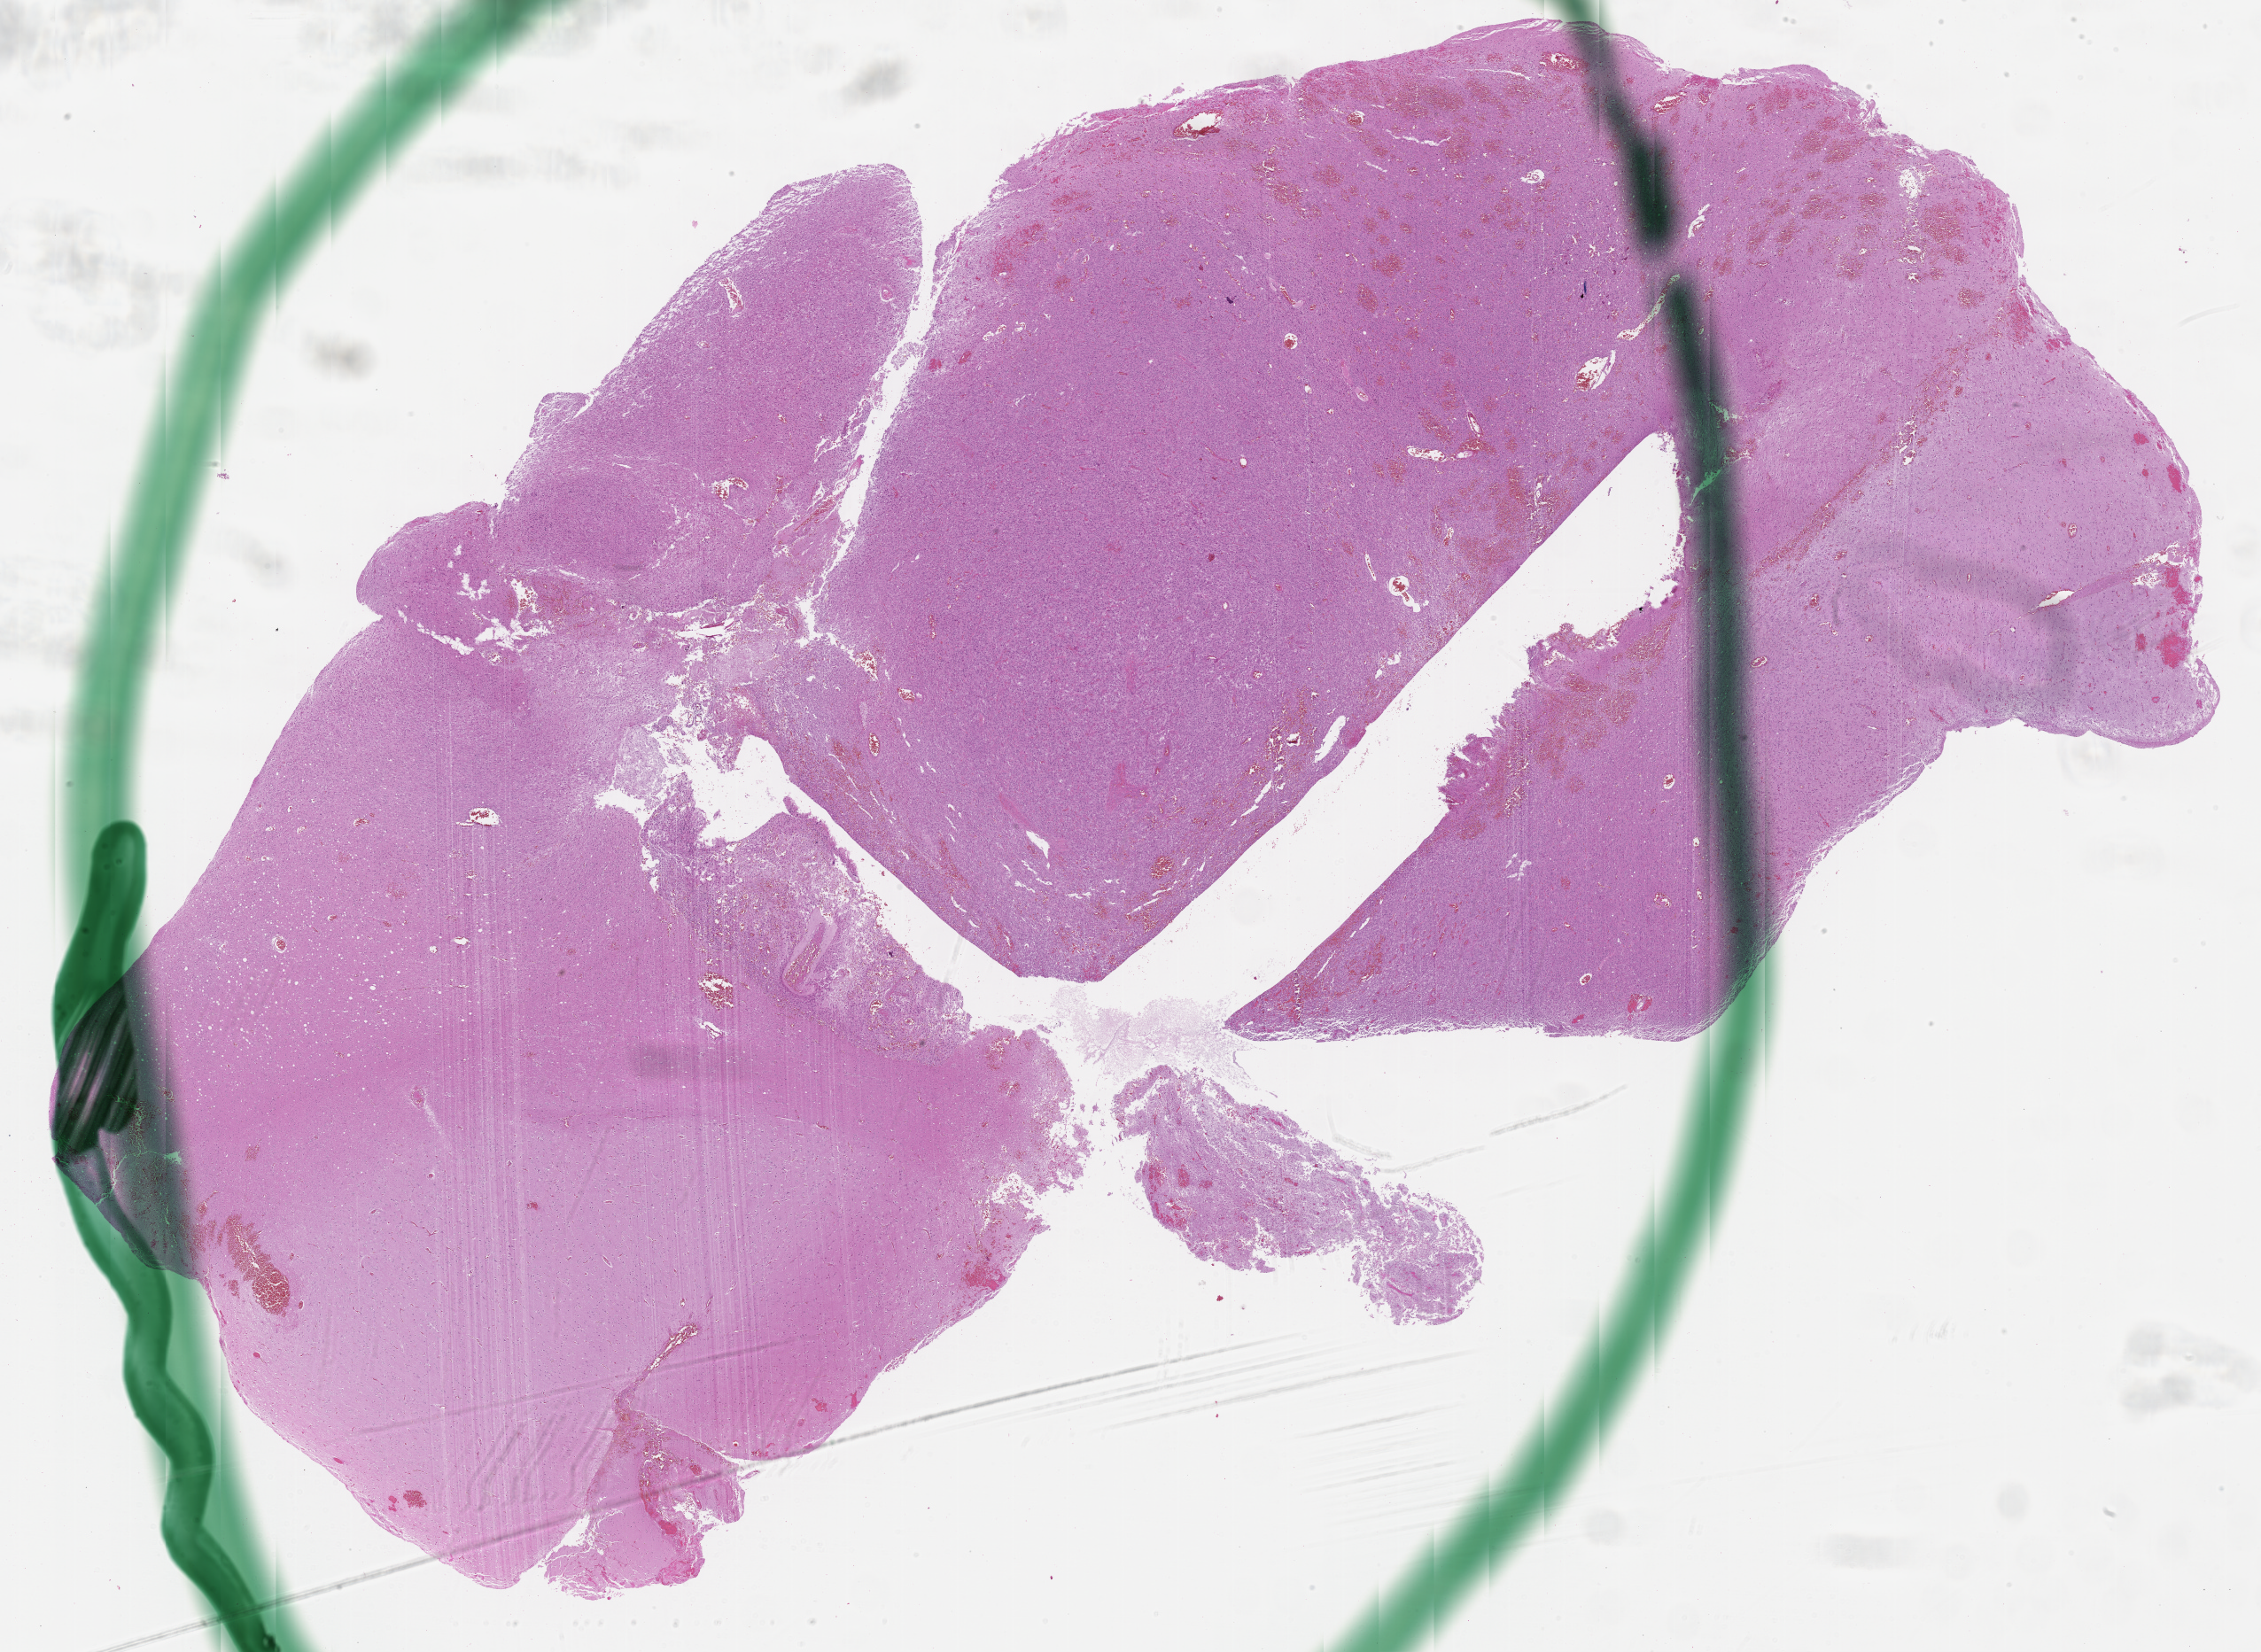
Whole-slide histology image, H&E — whole scanned area (about 20.7 x 15.1 mm, slide scanned at 40x) shown as a low-resolution overview; formalin-fixed paraffin-embedded (FFPE) diagnostic section; primary tumour sample from the brain. Male patient; age at initial diagnosis 50 years.
Histologic diagnosis: Glioblastoma.